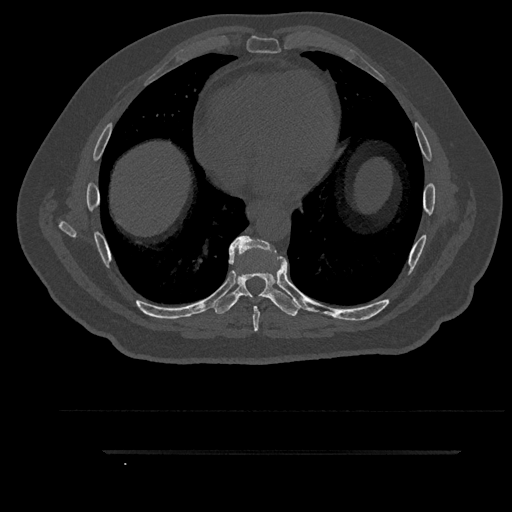
CT including the spine, one axial slice. Position 497 of 797 along the scan axis. Reconstruction kernel Br40s/3. Bone window (W 1800 / L 400 HU). 512 × 512 image matrix, field of view 432 × 432 mm. Male patient, age 63 years. From the clinical record (not read from this slice): primary cancer: renal; vertebrae with lytic lesions (as recorded): T8.
Annotated regions visible in this slice (semi-automatically segmented with operator editing):
- T6 vertebra: bounding box (x1, y1, x2, y2) in pixels: (251, 295, 253, 297)
- T7 vertebra: (229, 236, 286, 332)
- T8 vertebra: (211, 246, 300, 316)